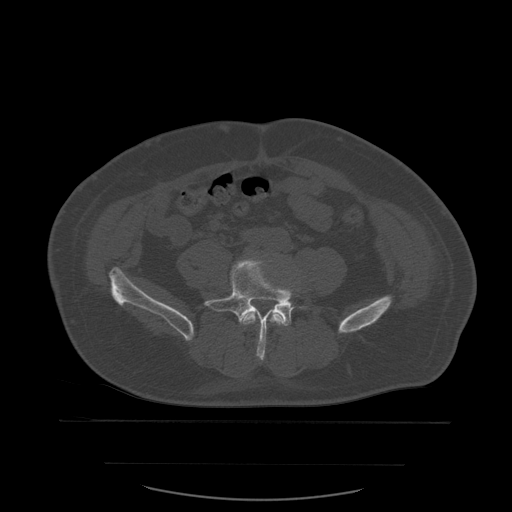
CT including the spine, one axial slice. Position 146 of 590 along the scan axis. Bone window (W 1800 / L 400 HU). 1.25 mm slice thickness. 512 × 512 image matrix, field of view 479 × 479 mm. Patient age 71 years. From the clinical record (not read from this slice): primary cancer: lung.
Outlined on this slice (semi-automatic segmentation, software-assisted and operator-edited):
- L4 vertebra: bounding box [x1, y1, x2, y2] px = [241, 312, 284, 325]
- L5 vertebra: [204, 257, 321, 361]